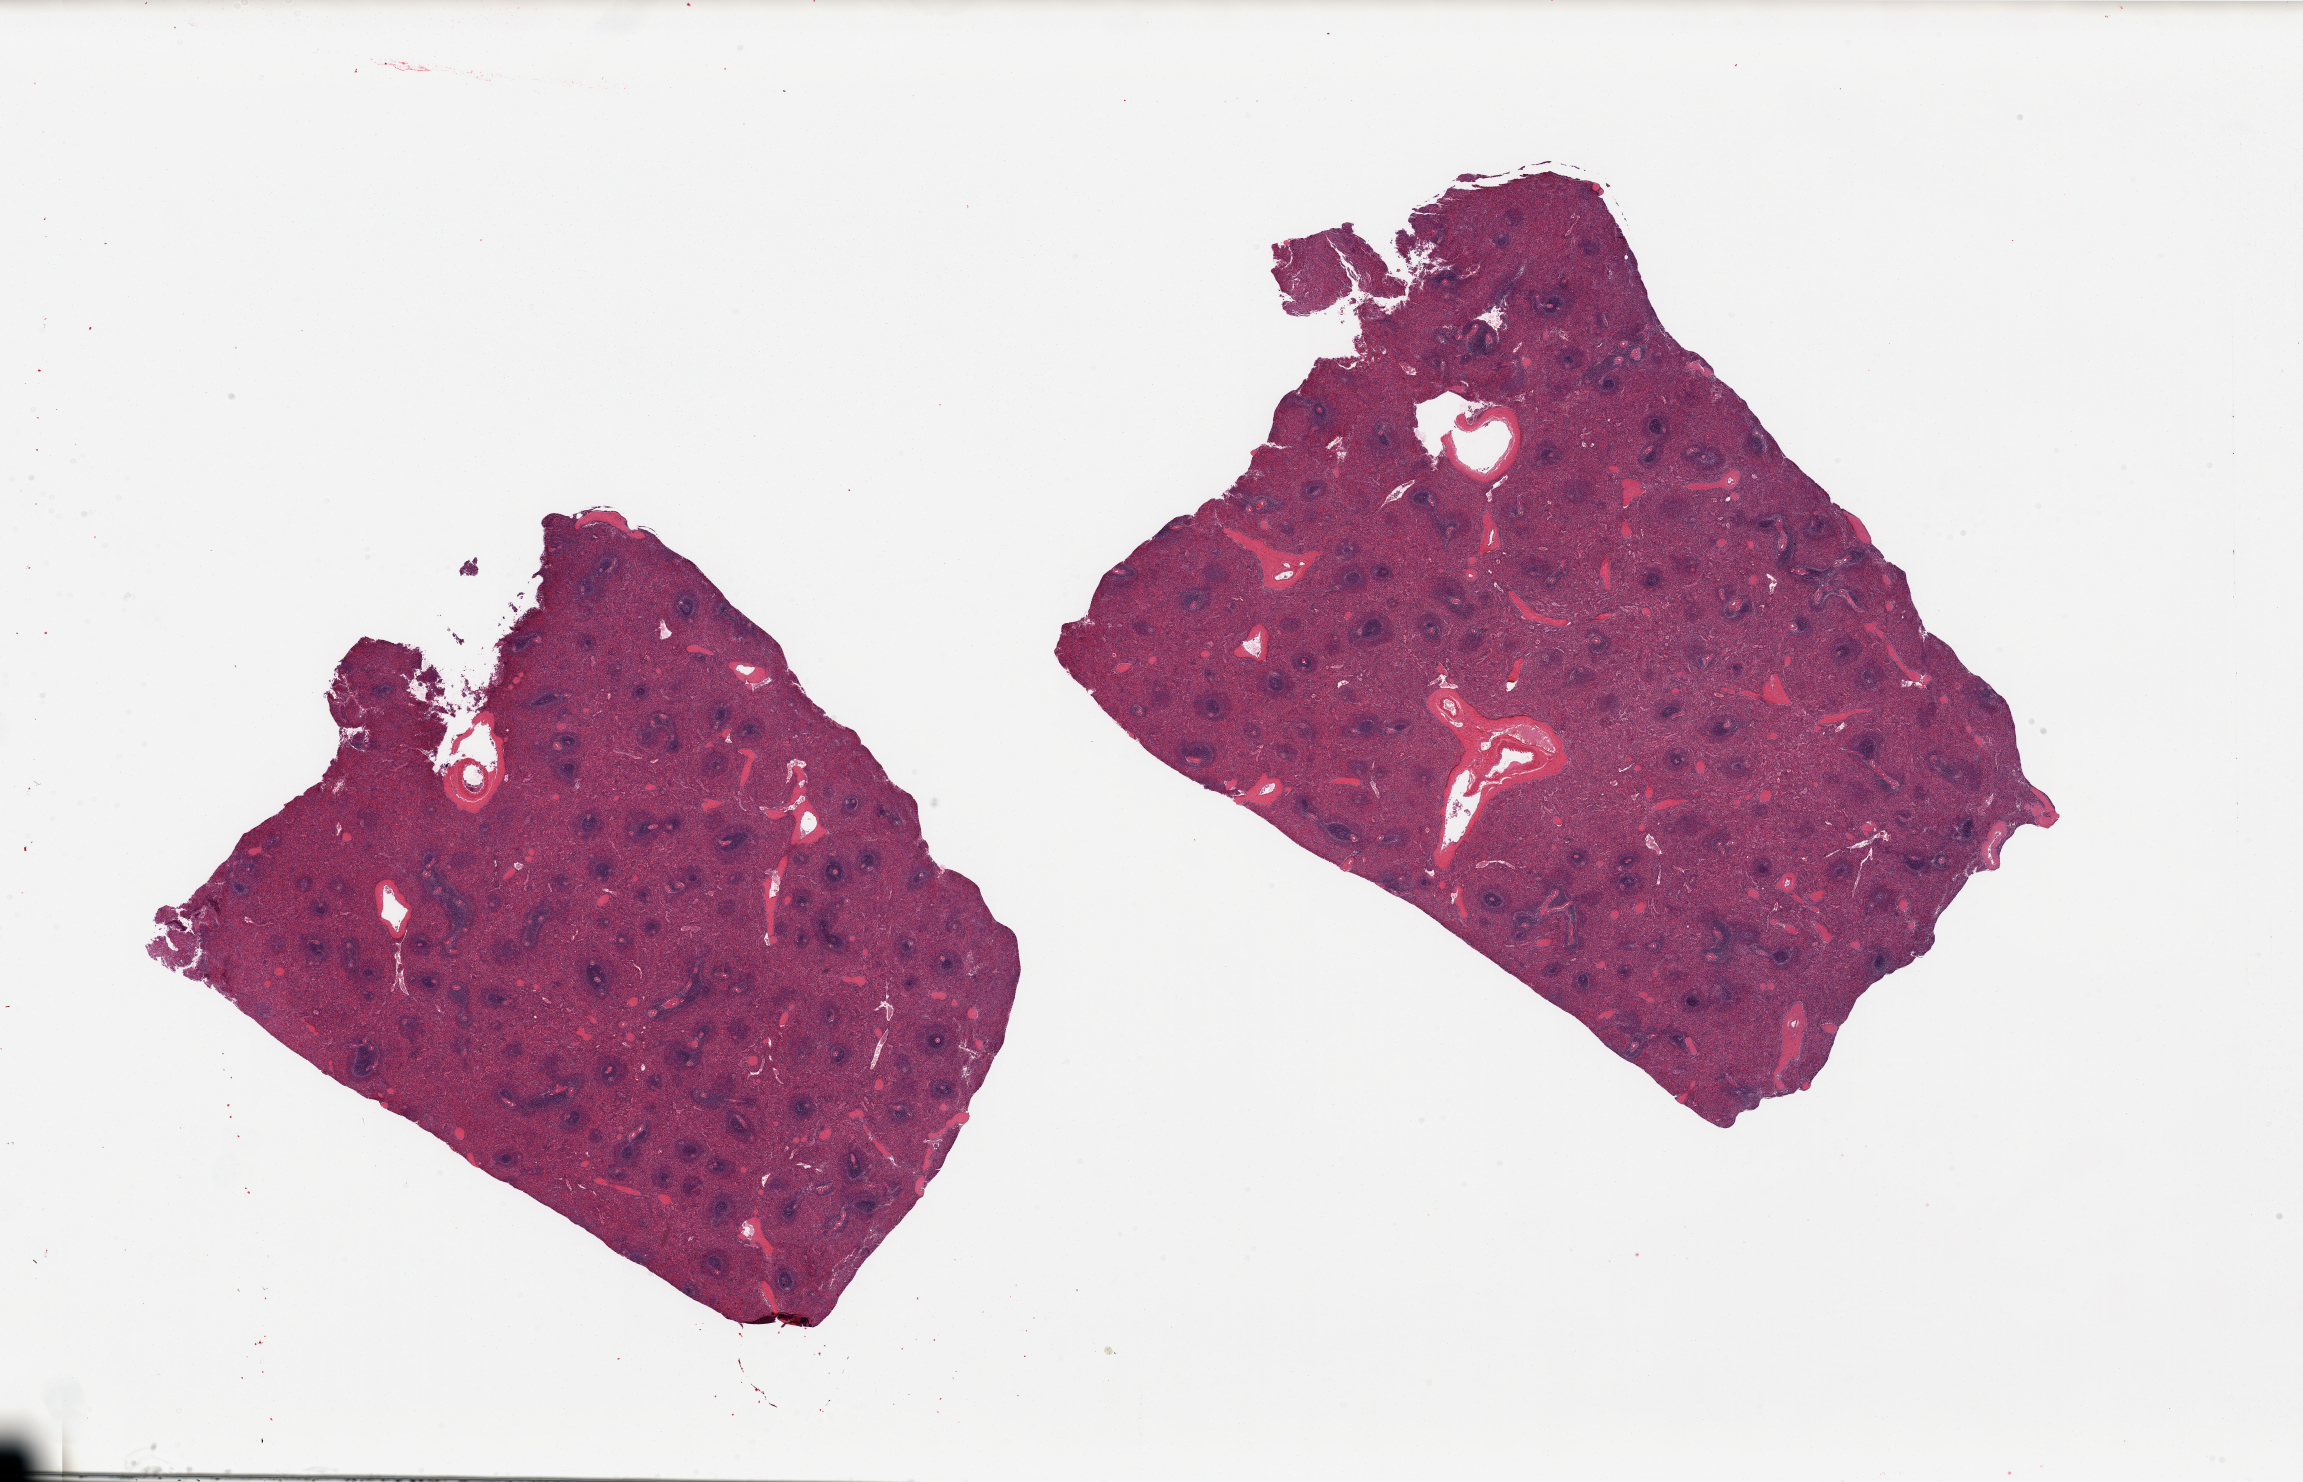
H&E whole-slide image, brightfield — low-resolution overview of the scanned area, about 36.4 x 23.4 mm (slide scanned at 20x). PAXgene-fixed paraffin-embedded (PFPE) section. Sampled site (target tissue): spleen. Tissue donor sample.
Reviewer comment on this tissue sample: 2 pieces, mild congestion.